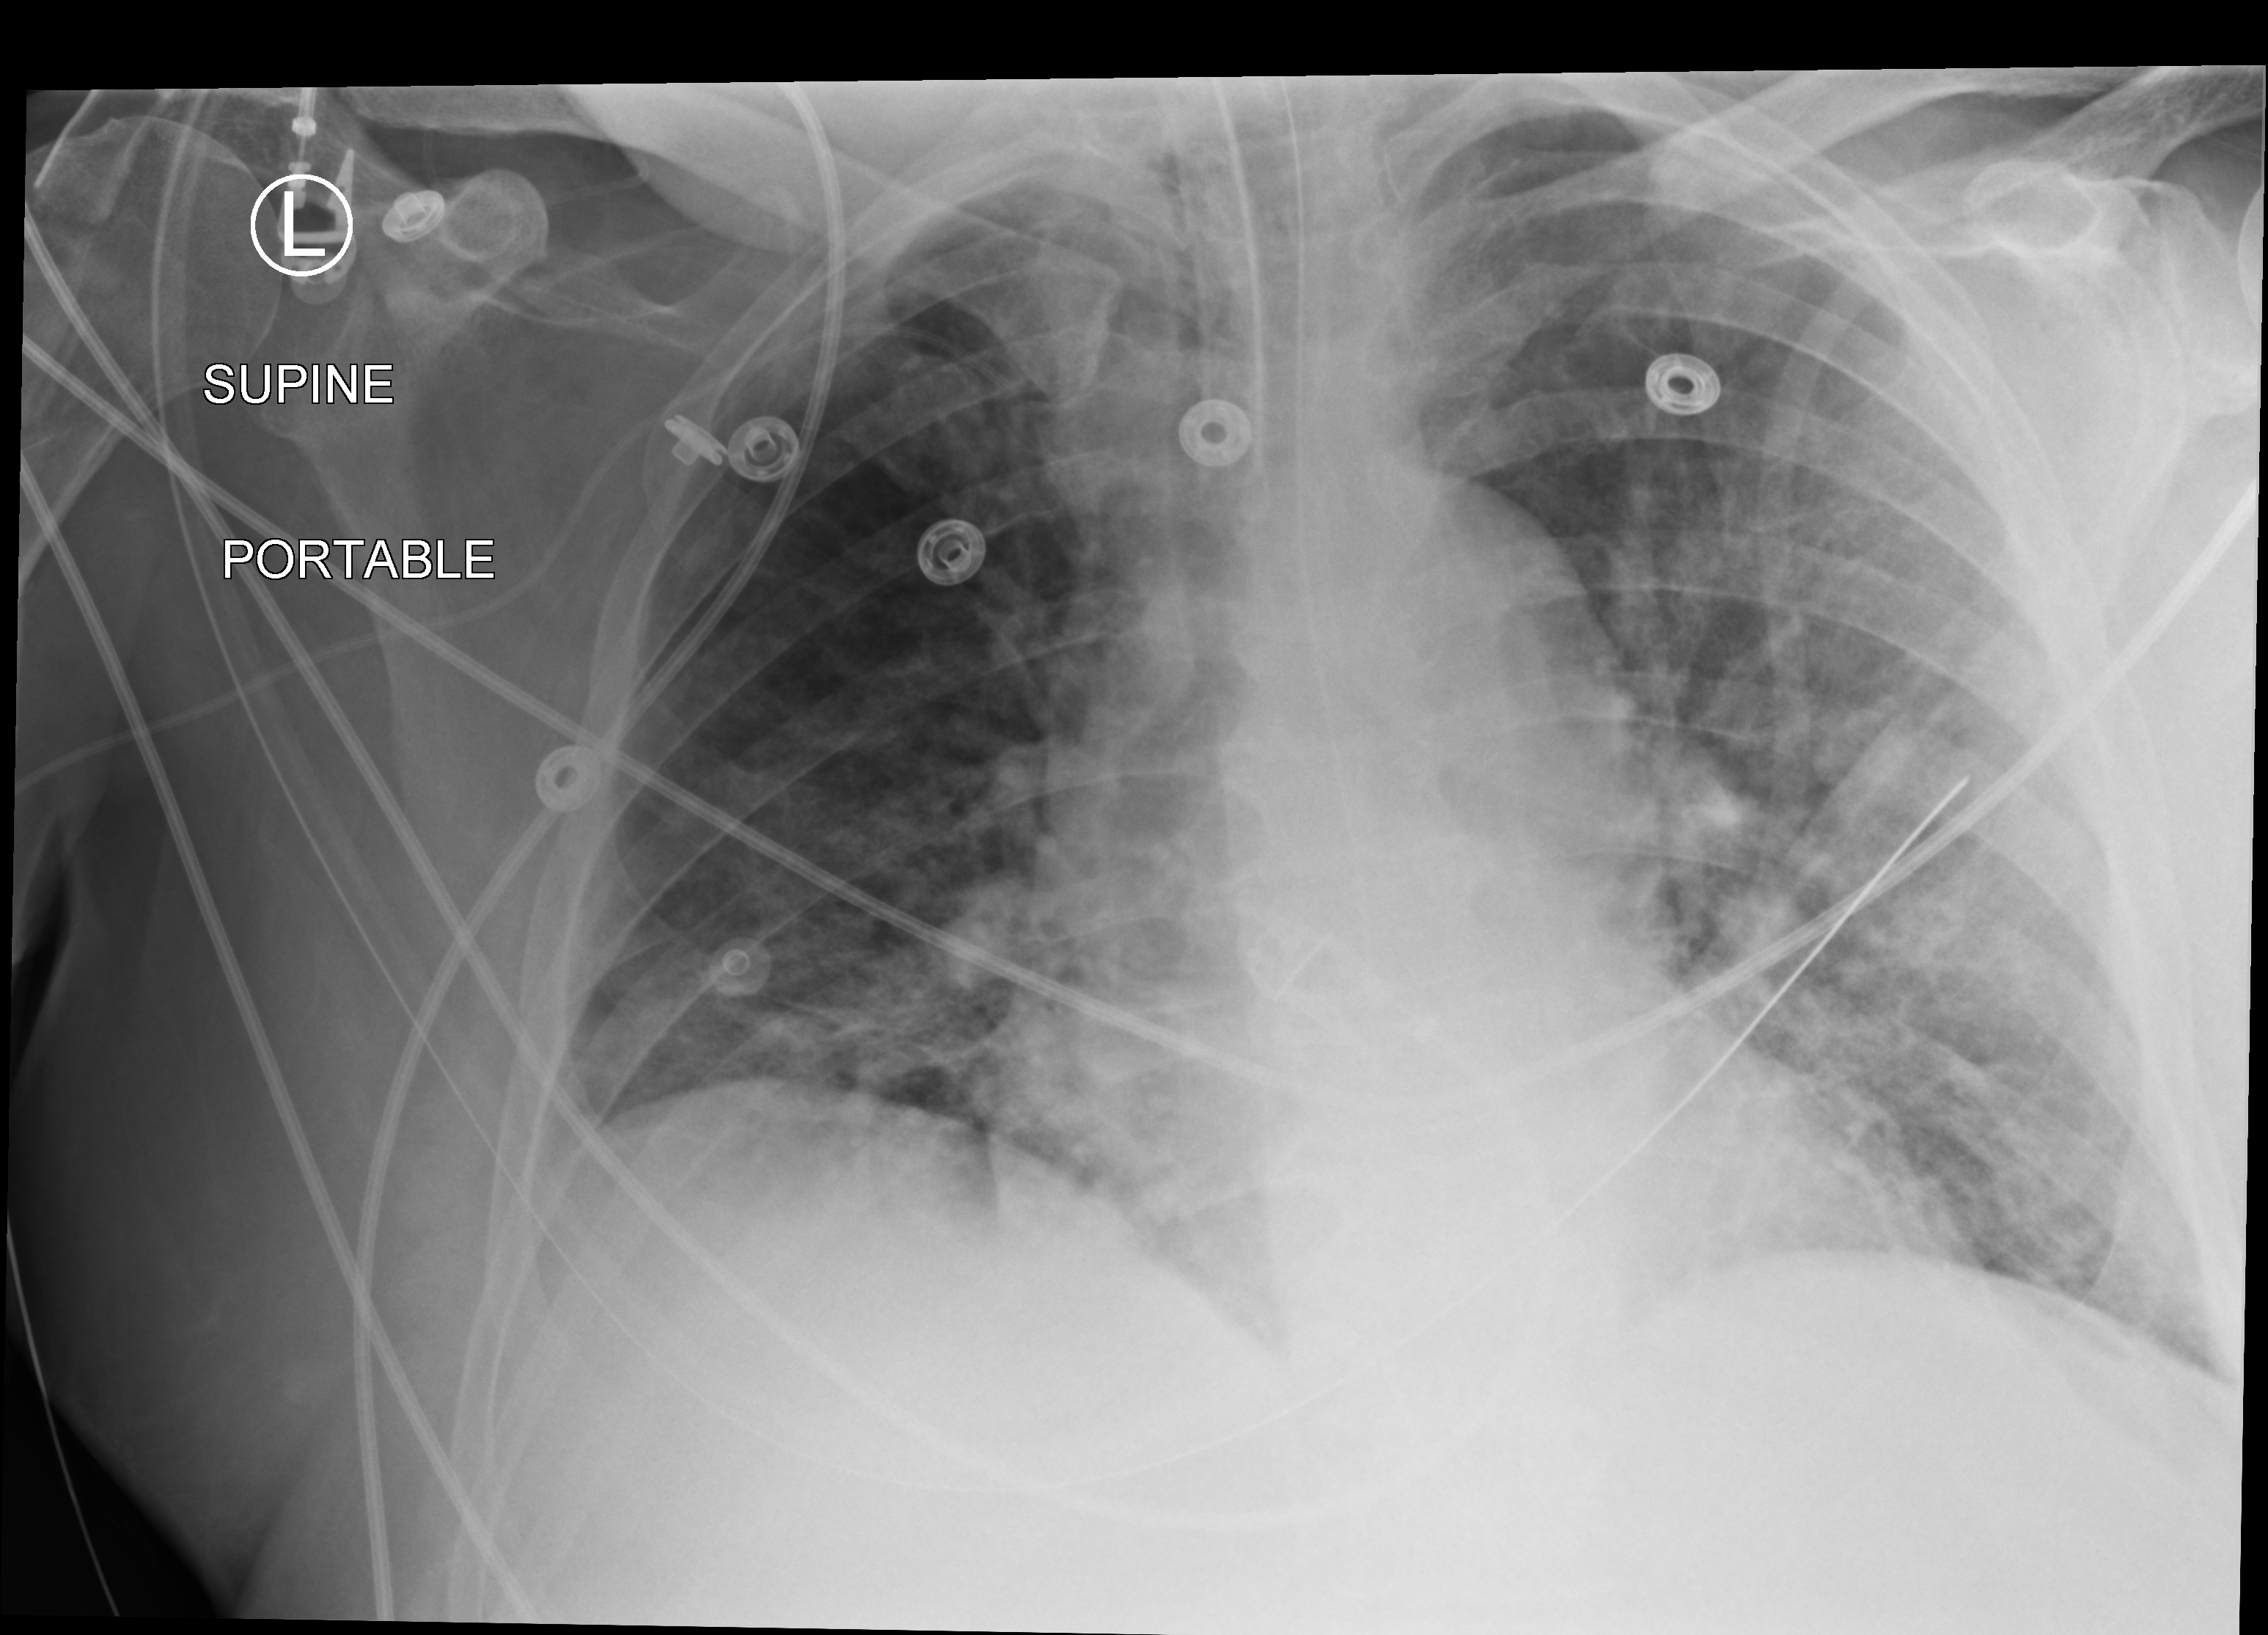
Bedside chest radiograph (computed radiography); anteroposterior (AP) projection. Male patient hospitalised with COVID-19, age 60–74 years.
Hospital-stay facts (about this admission, not read from this image; timing relative to this image not recorded):
- length of hospital stay: 26 days
- mechanically ventilated during this hospital stay: yes